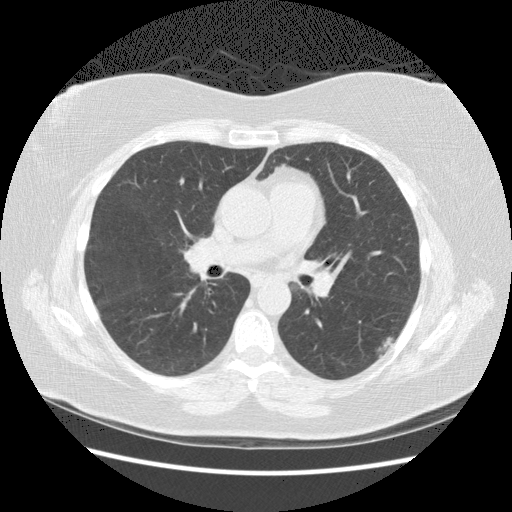
Chest CT (low-dose screening protocol), one axial image, second annual screen, lung window (W 1500 / L -600 HU), 2.5 mm slice thickness, 120 kVp, slice 77 of 140 in the series. Female, age 57 years at enrolment. Current smoker at enrolment.
Expert reader's lesion annotation, bounding box (x1, y1, x2, y2) in pixels: (364, 329, 402, 366). Screening reader's record for this exam (one nodule recorded; not confirmed to be the boxed lesion): non-calcified nodule or mass ≥4 mm, left lower lobe, 19 × 9 mm, poorly defined margins, mixed attenuation, pre-existing on the prior screen: yes; interval growth: yes. Official screen result: positive, other. Participant outcome: lung cancer diagnosed 560 days after this screen (after the third annual screen) — squamous cell carcinoma, NOS, left lower lobe, poorly differentiated (G3), stage IB (AJCC 6th edition), 40 mm at pathology.